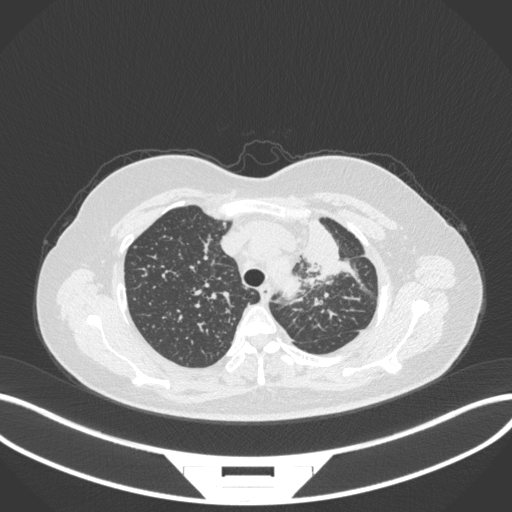
Chest CT, one axial slice; slice 261 of 348 in the series (ordered by position); reconstruction kernel B31f; lung window (W 1500 / L -600 HU); 1 mm slice thickness; 512 × 512 image matrix. Female patient, age 49 years. From the clinical record (not read from this slice): clinical TNM (as recorded): T1c N0 M1.
Structures marked on this image (bounding box drawn by a radiologist):
- lung tumour (recorded histology: adenocarcinoma): bounding box (x1, y1, x2, y2) in pixels: (301, 209, 344, 282)